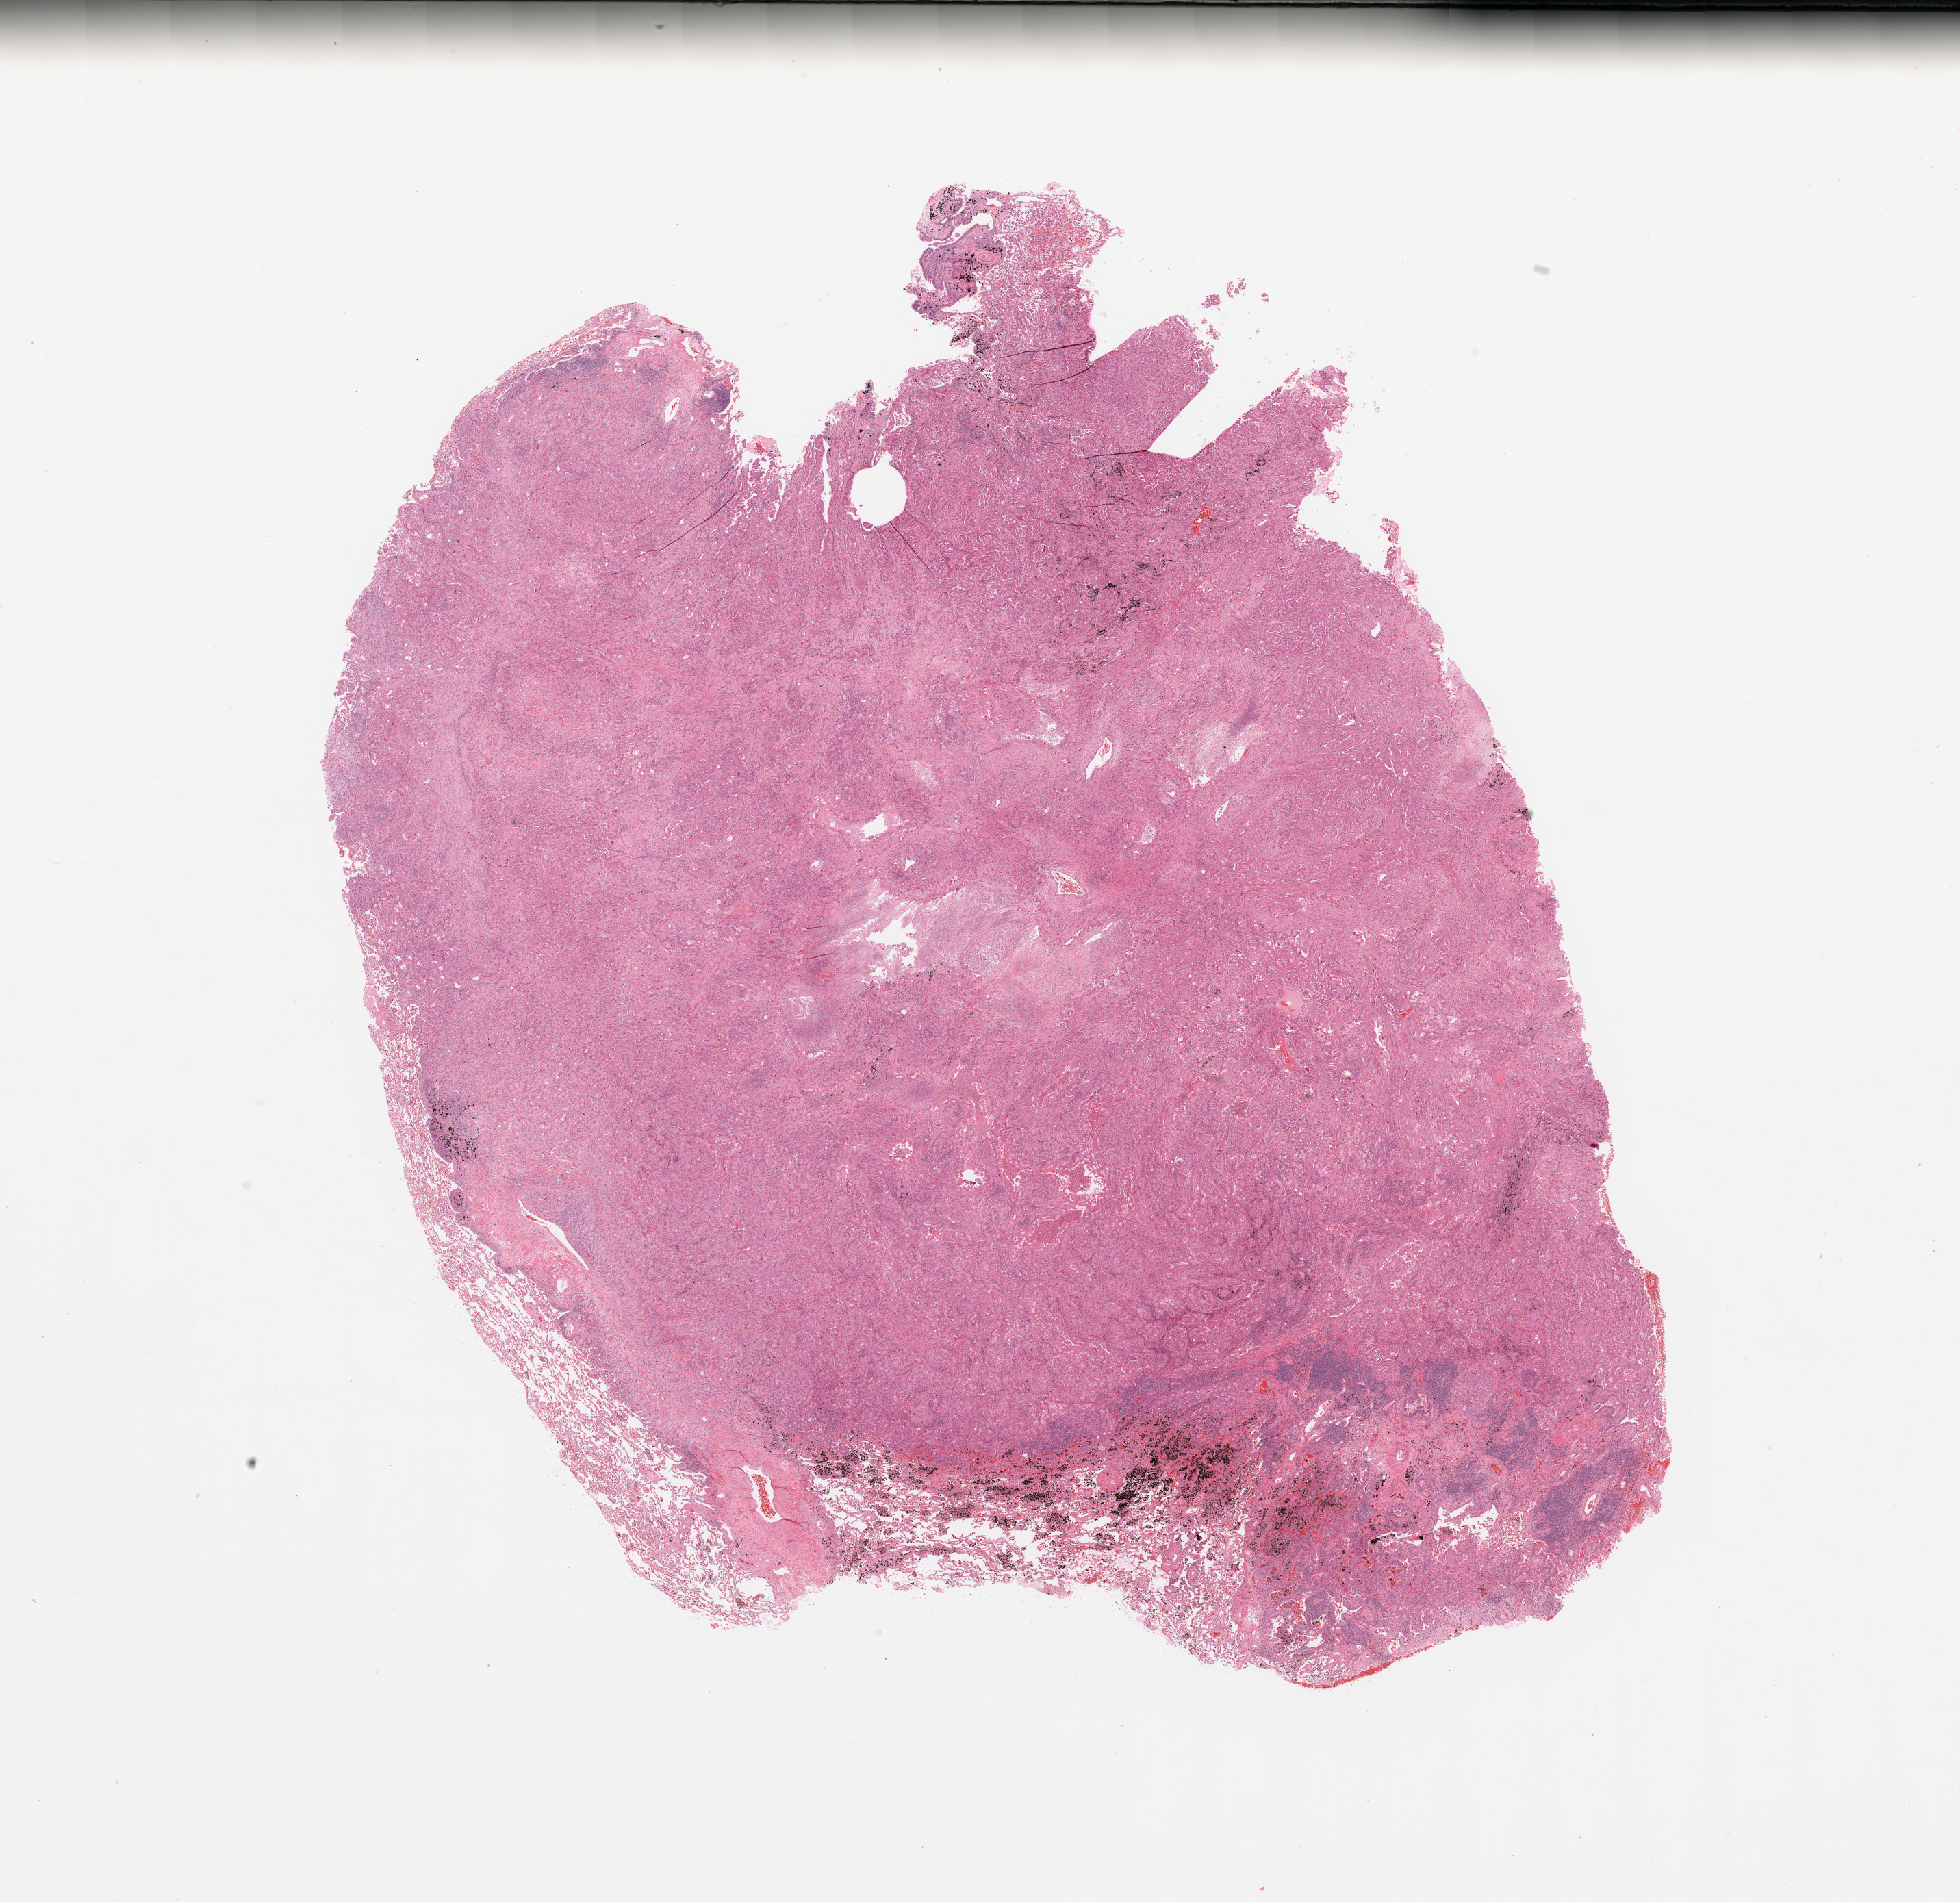
Hematoxylin and eosin (H&E) stained whole-slide image, a low-resolution overview of the entire scanned area, about 22.6 x 22.0 mm (acquisition: 20x scan); lung, tumour tissue. 71-year-old male patient. Histologic grade: G3 (poorly differentiated).
* diagnosis: Adenocarcinoma, NOS
* AJCC pathologic stage: IIIA